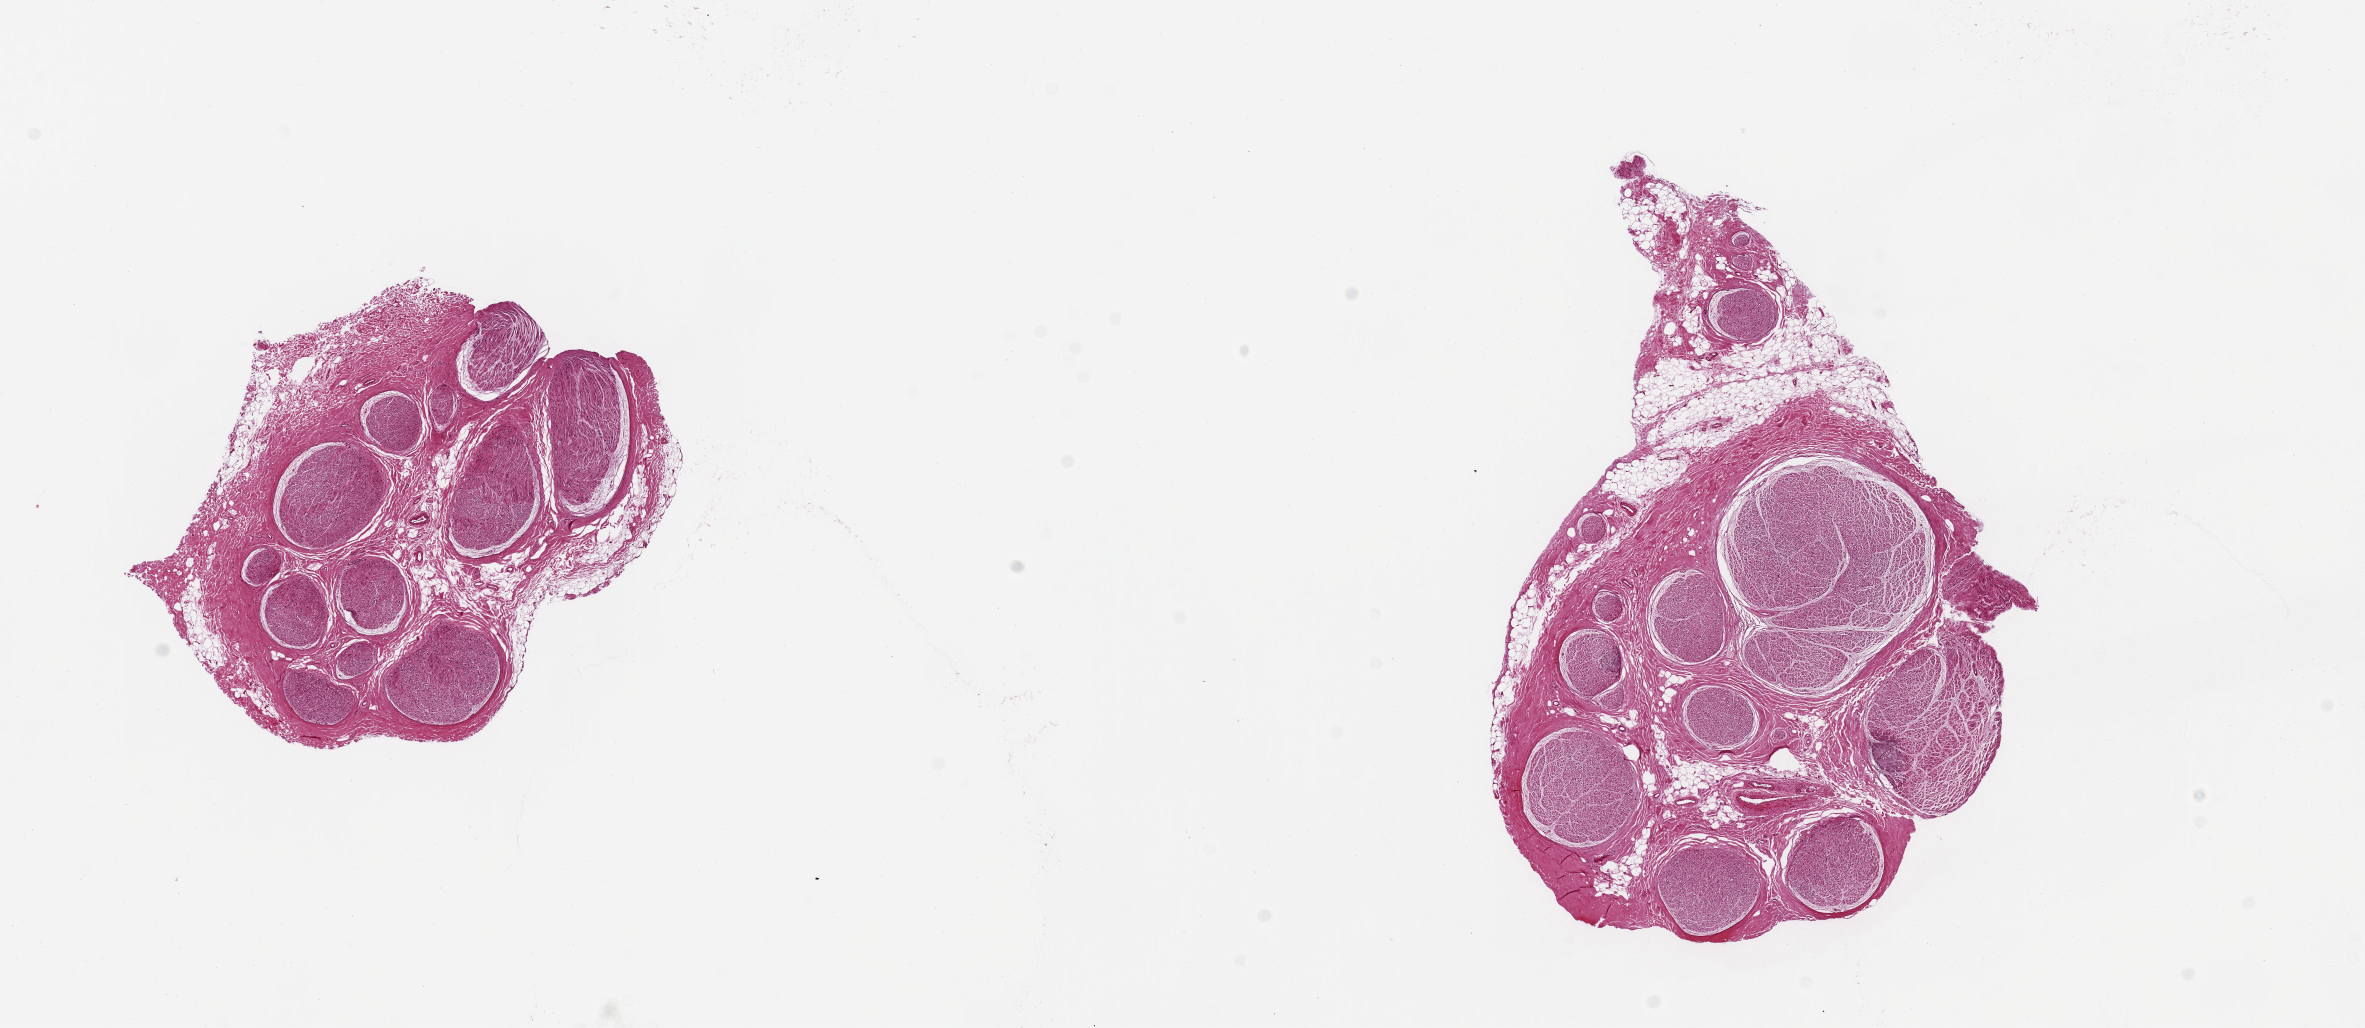
Hematoxylin and eosin (H&E) whole-slide image, low-resolution overview of the scanned area, about 18.7 x 8.1 mm; PAXgene-fixed, paraffin-embedded tissue; section of tibial nerve (target tissue); tissue donor sample. Male donor.
* review note (as recorded): 2 pieces, 4x3.5 & 6x4mm; ~10% adipose in and around each